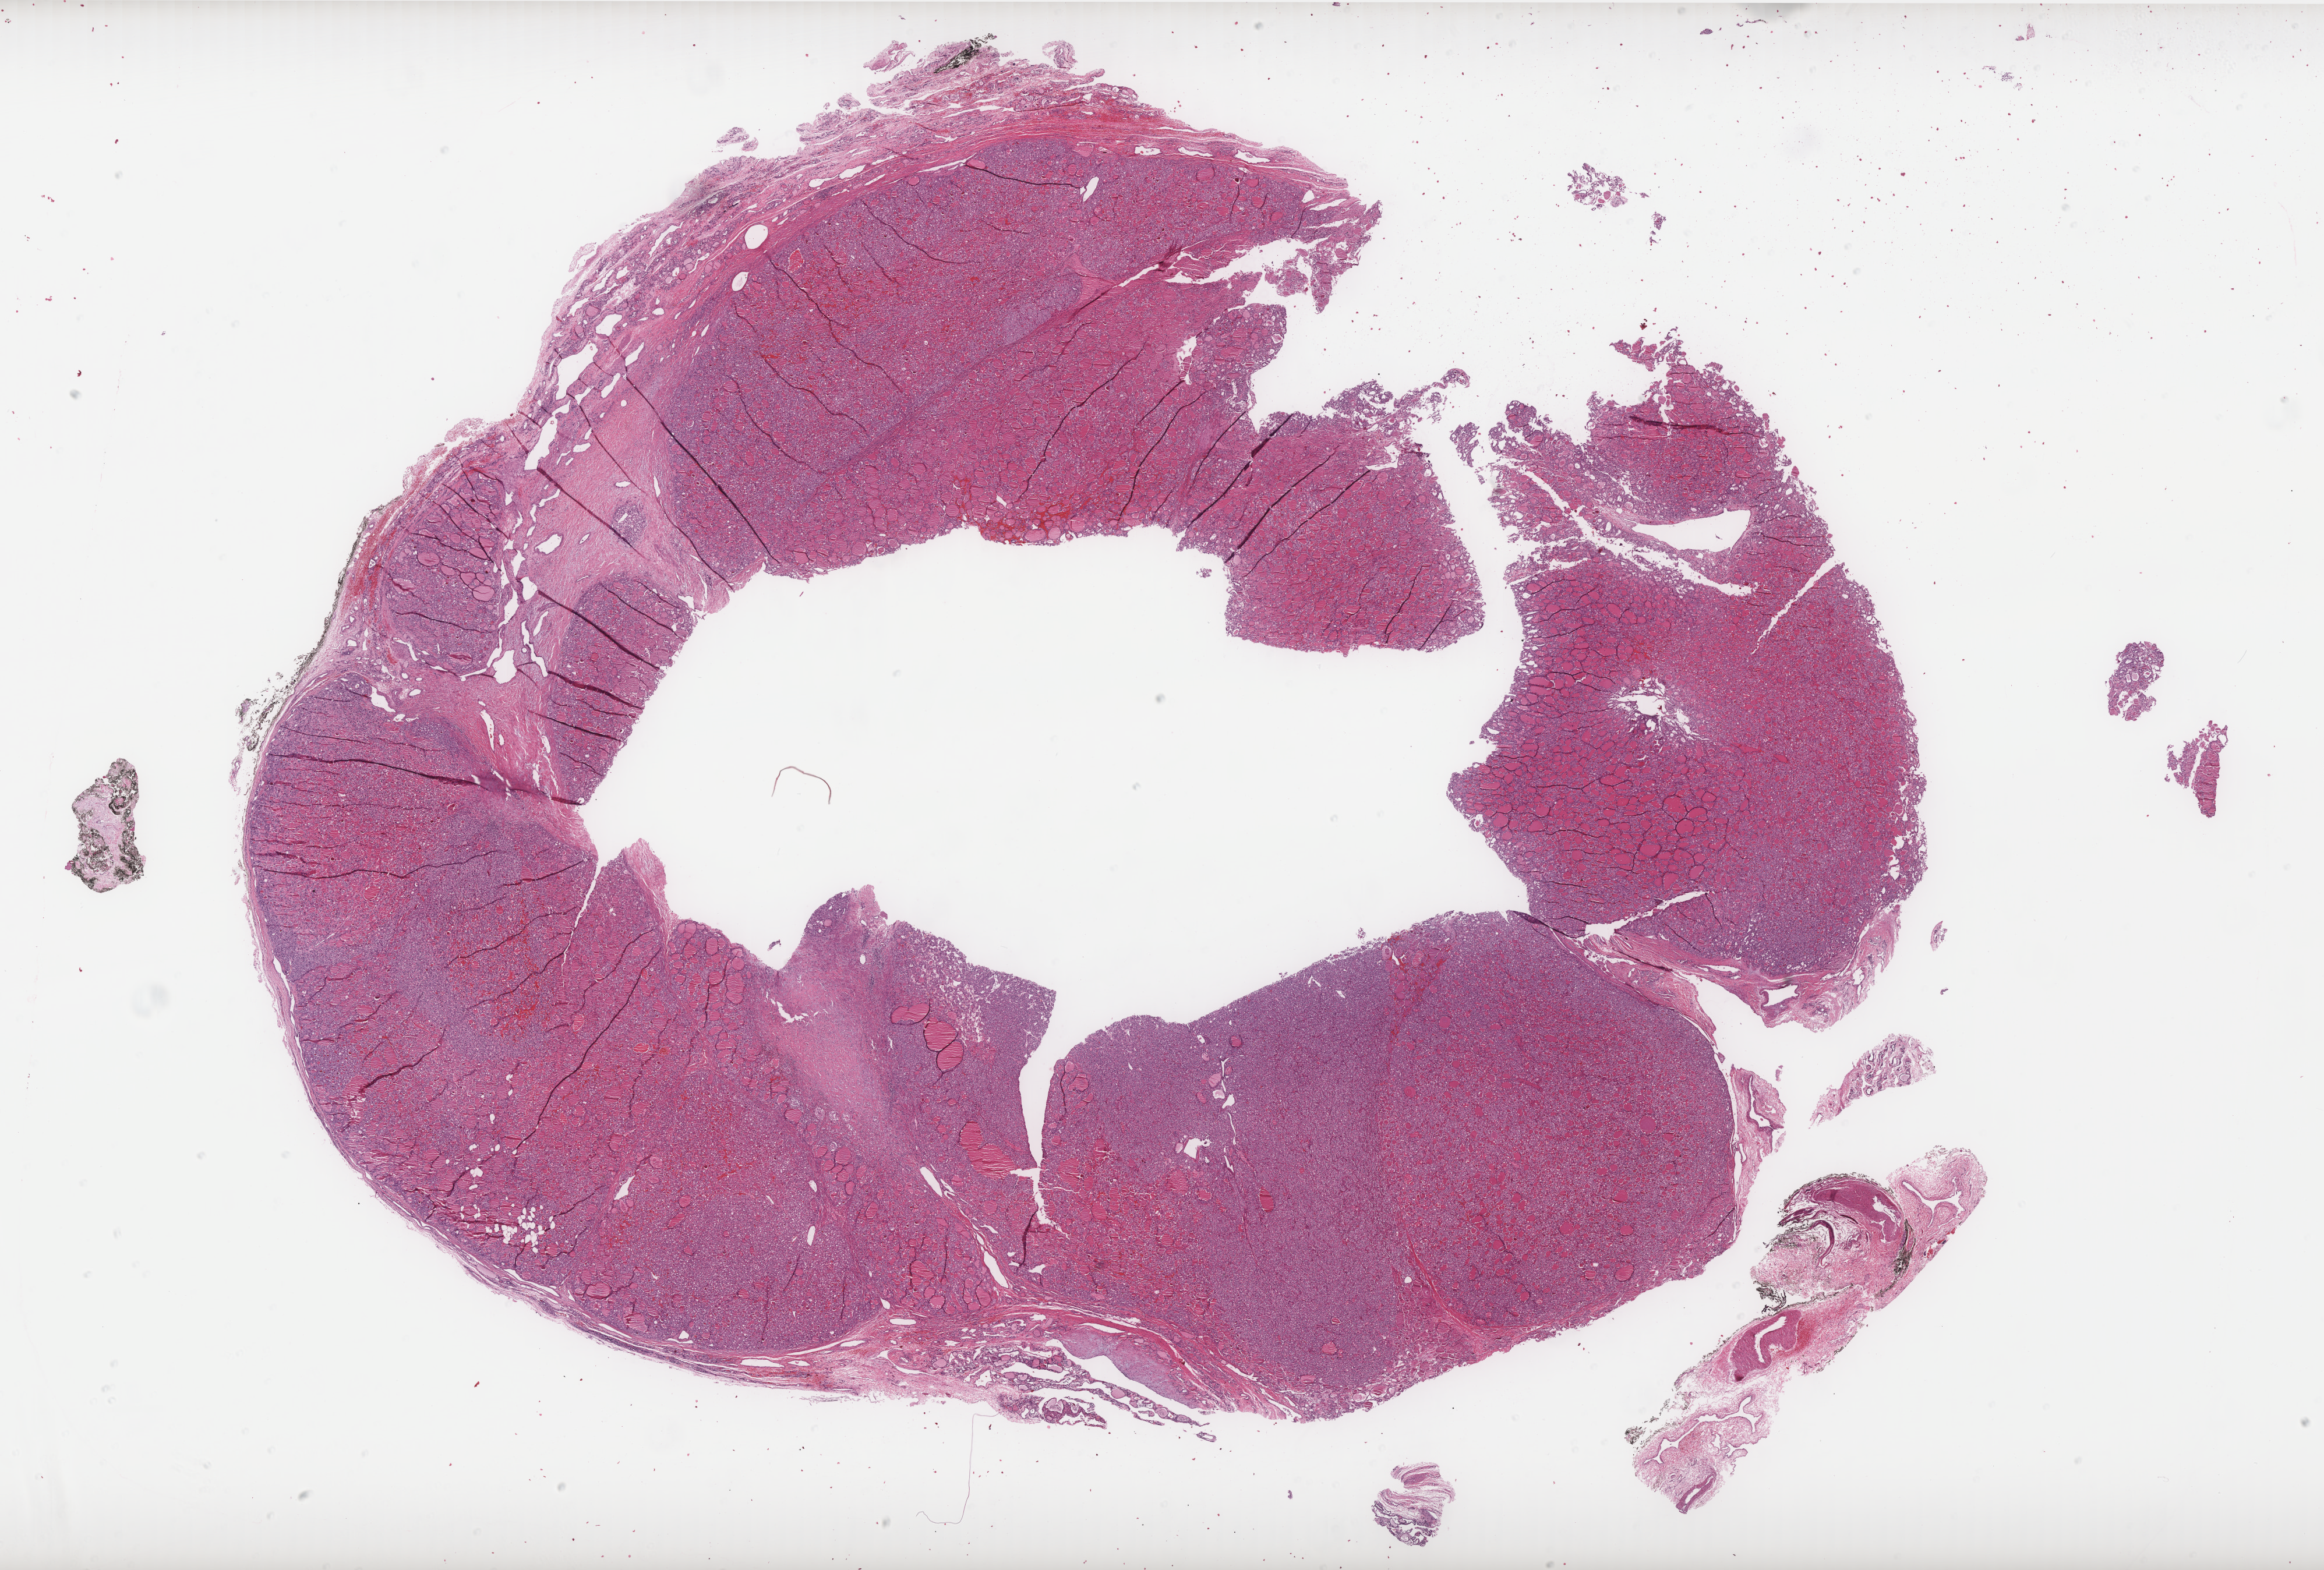
Digitized H&E tissue section (whole slide), low-resolution overview of the scanned area, about 32.0 x 21.6 mm (from a 40x scan); FFPE section; sample: primary tumour, thyroid. Patient: male, age at initial diagnosis 65 years.
- laterality: right
- AJCC pathologic stage: II (6th edition)
- diagnosis: Papillary adenocarcinoma, NOS (thyroid gland)